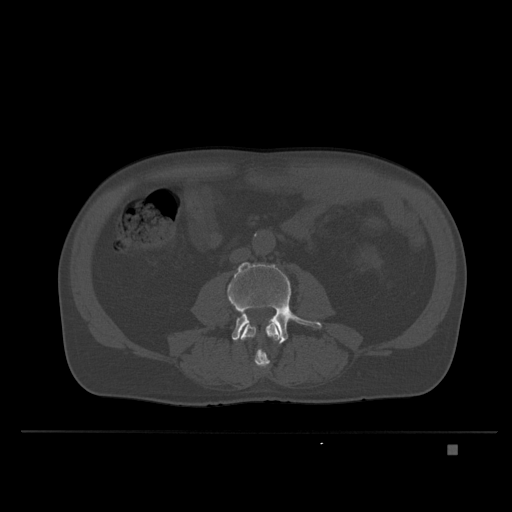
CT including the spine, one axial slice; slice 84 of 435 in the series (ordered by position); bone window (W 1800 / L 400 HU); 512 × 512 image matrix. Male patient, age 73 years. From the clinical record (not read from this slice): primary cancer: skin.
Outlined on this slice (semi-automatic segmentation, software-assisted and operator-edited):
- L3 vertebra: bounding box [x1, y1, x2, y2] px = [240, 321, 281, 369]
- L4 vertebra: [227, 262, 322, 345]